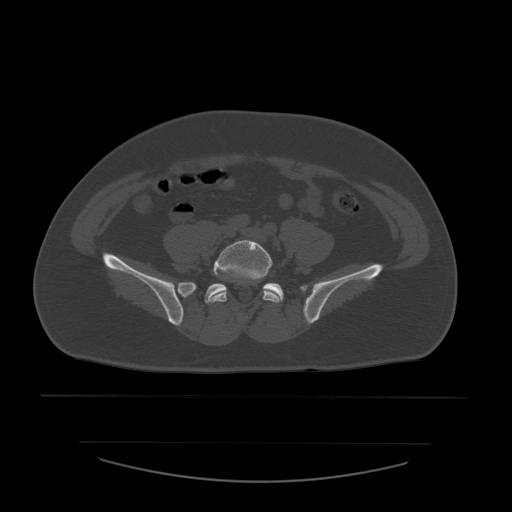
CT including the spine, one axial slice. Position 112 of 532 along the scan axis. Reconstruction kernel STANDARD. Bone window (W 1800 / L 400 HU). 1.25 mm slice thickness. 512 × 512 image matrix, field of view 441 × 441 mm. Patient age 44 years. From the clinical record (not read from this slice): primary cancer: soft tissue sarcoma.
Outlined on this slice (semi-automatically segmented with operator editing):
- L5 vertebra: bounding box <209,240,281,319> (left, top, right, bottom; pixels)